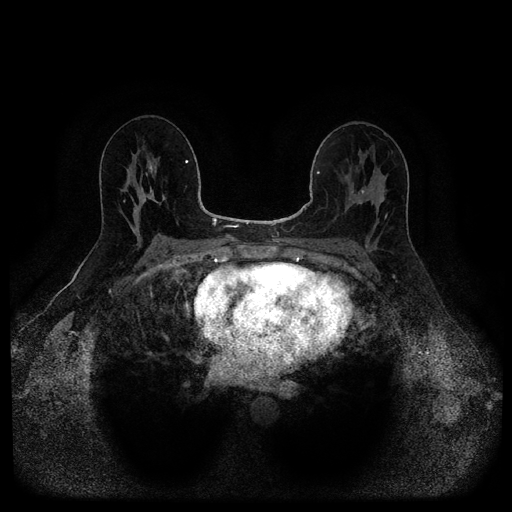
Breast MRI (dynamic contrast-enhanced, multi-phase), one axial slice. Slice 61 of 116 in the series (ordered by position). Dynamic contrast-enhanced series, time point 2 of 5 at this slice position (early post-contrast). 1.5 T. TE 2.6 ms, TR 5.3 ms. 2.2 mm slice thickness. 512 × 512 image matrix, field of view 350 × 350 mm. Patient: female, 49 years.
Outlined on this slice (semi-automatically segmented with operator editing):
- breast lesion (labelled benign in the annotation): bounding box <372,225,376,231> (left, top, right, bottom; pixels)